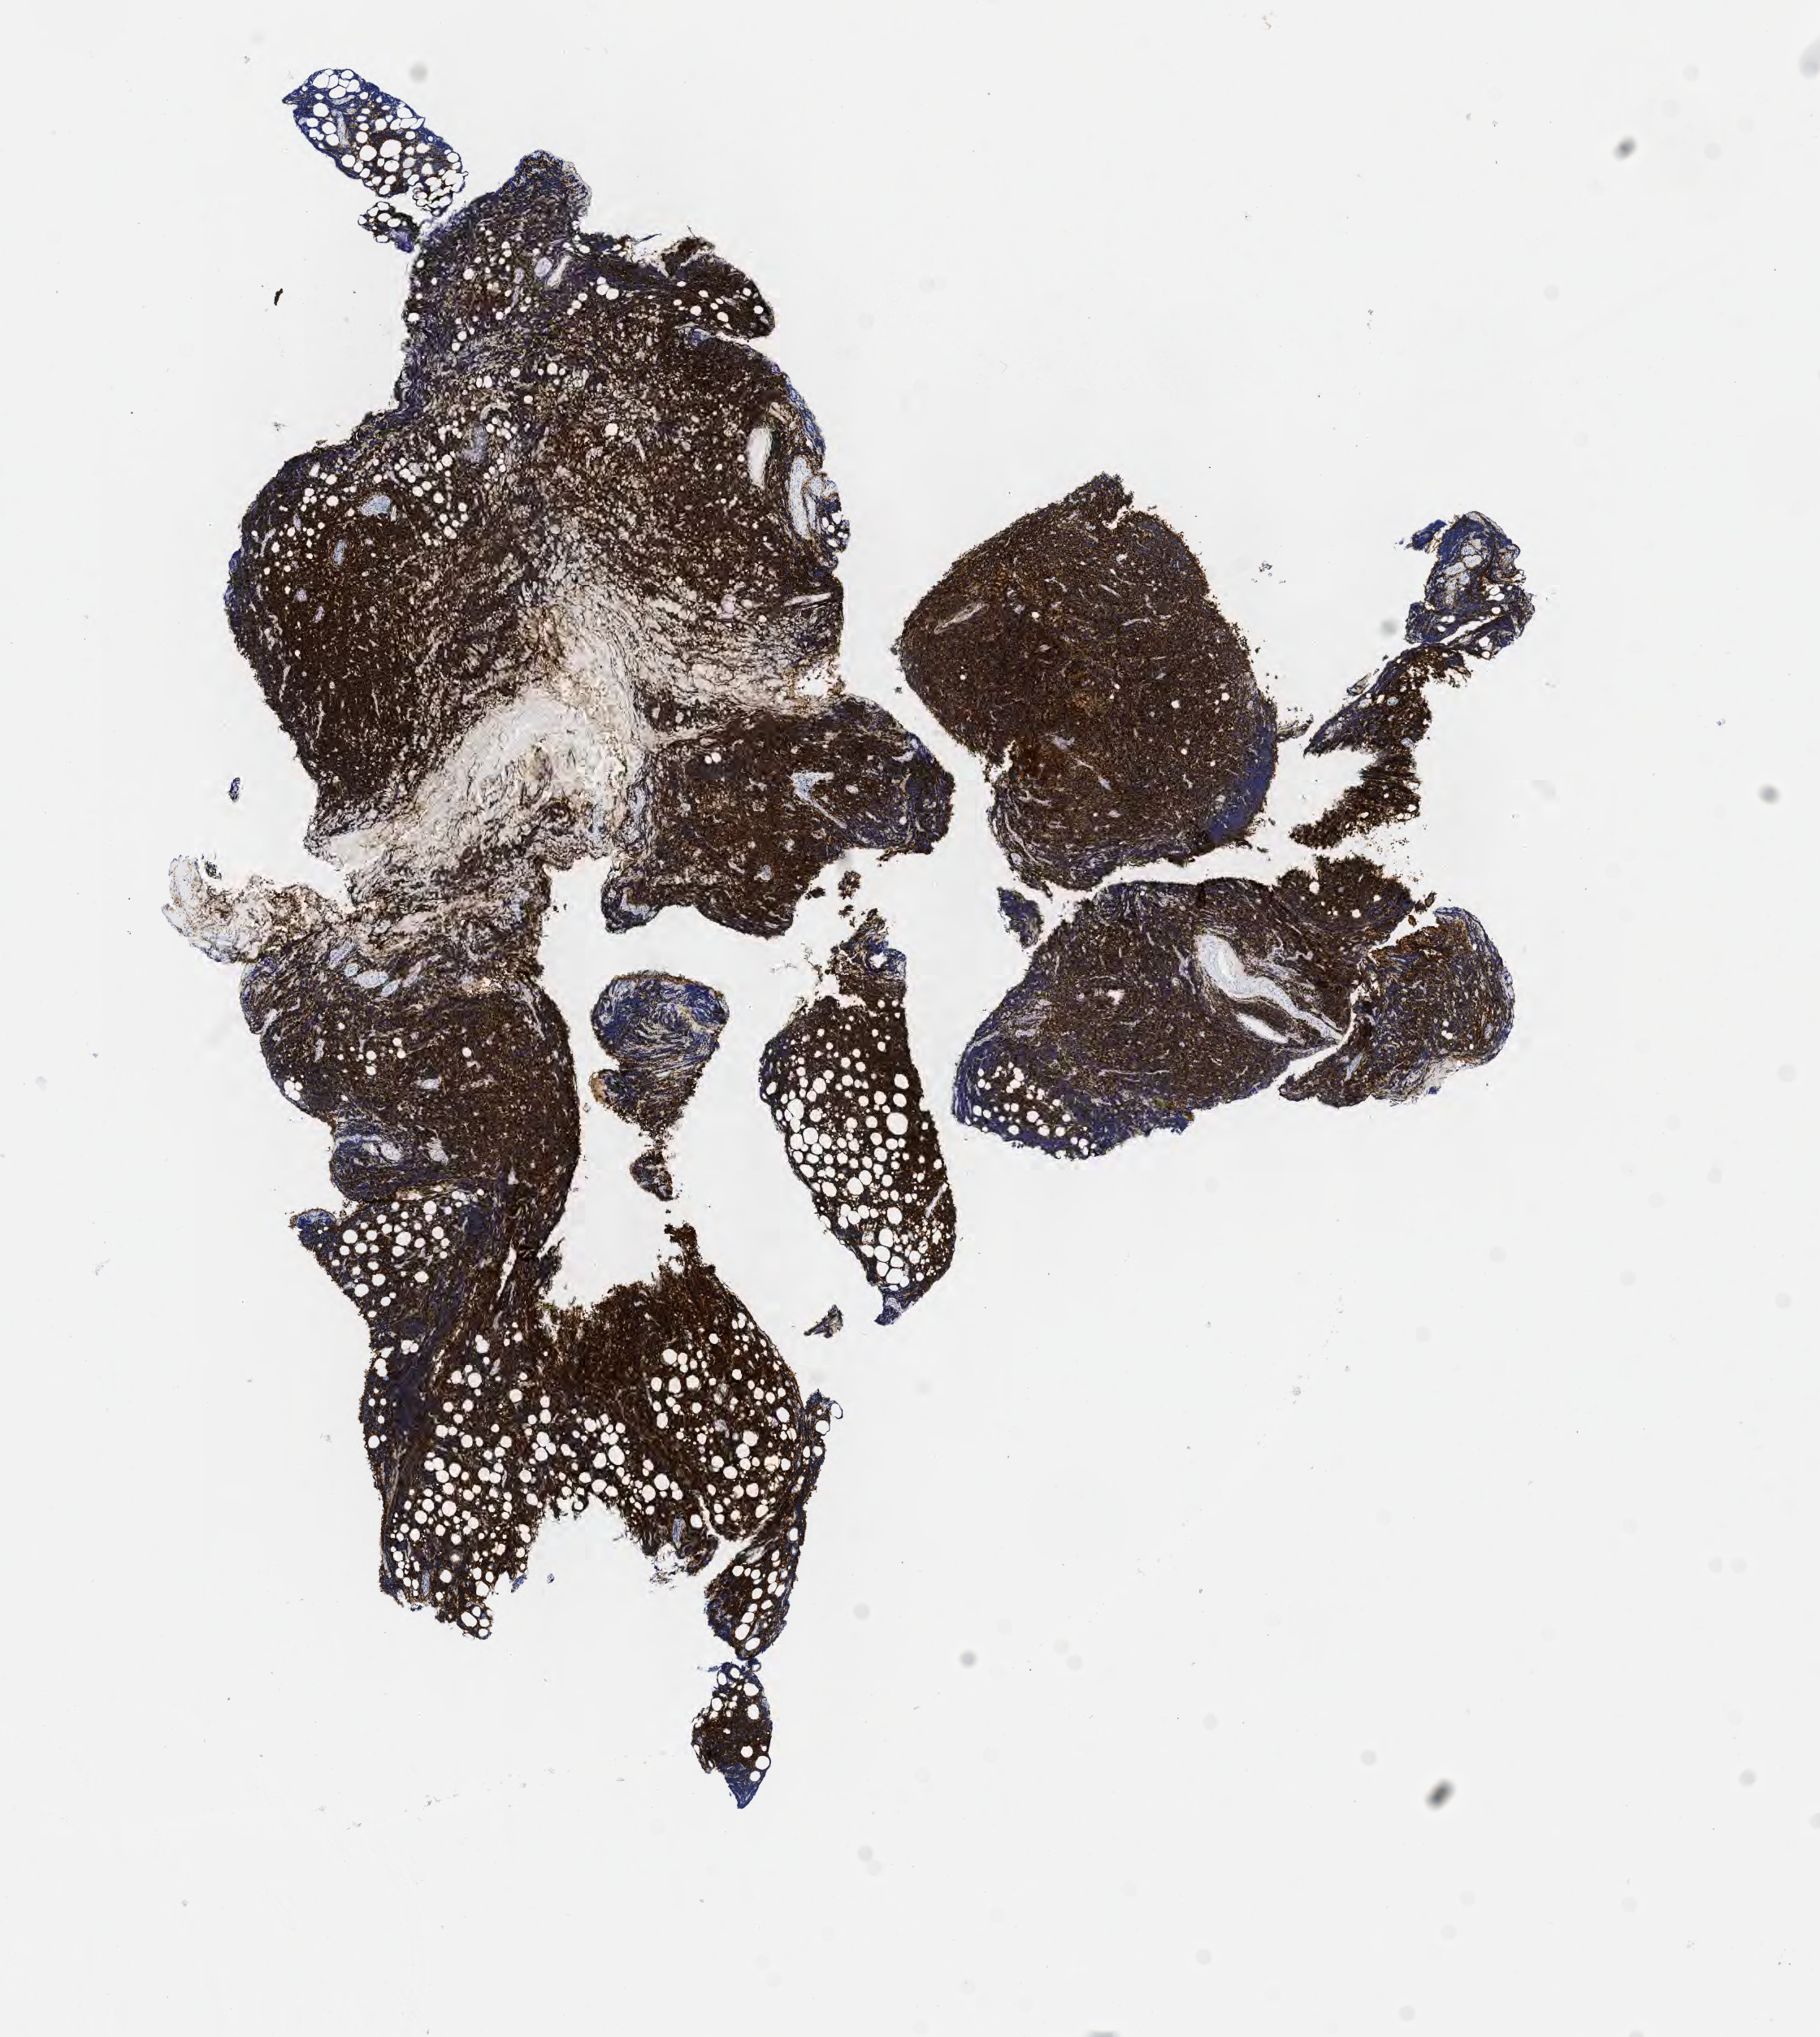
IHC for CD20, whole-slide image, whole scanned area (about 9.1 x 10.1 mm) shown as a low-resolution overview; tumor tissue; anatomic site: orbit. Male patient, 20 years old.
Histologic diagnosis: Burkitt lymphoma, NOS.